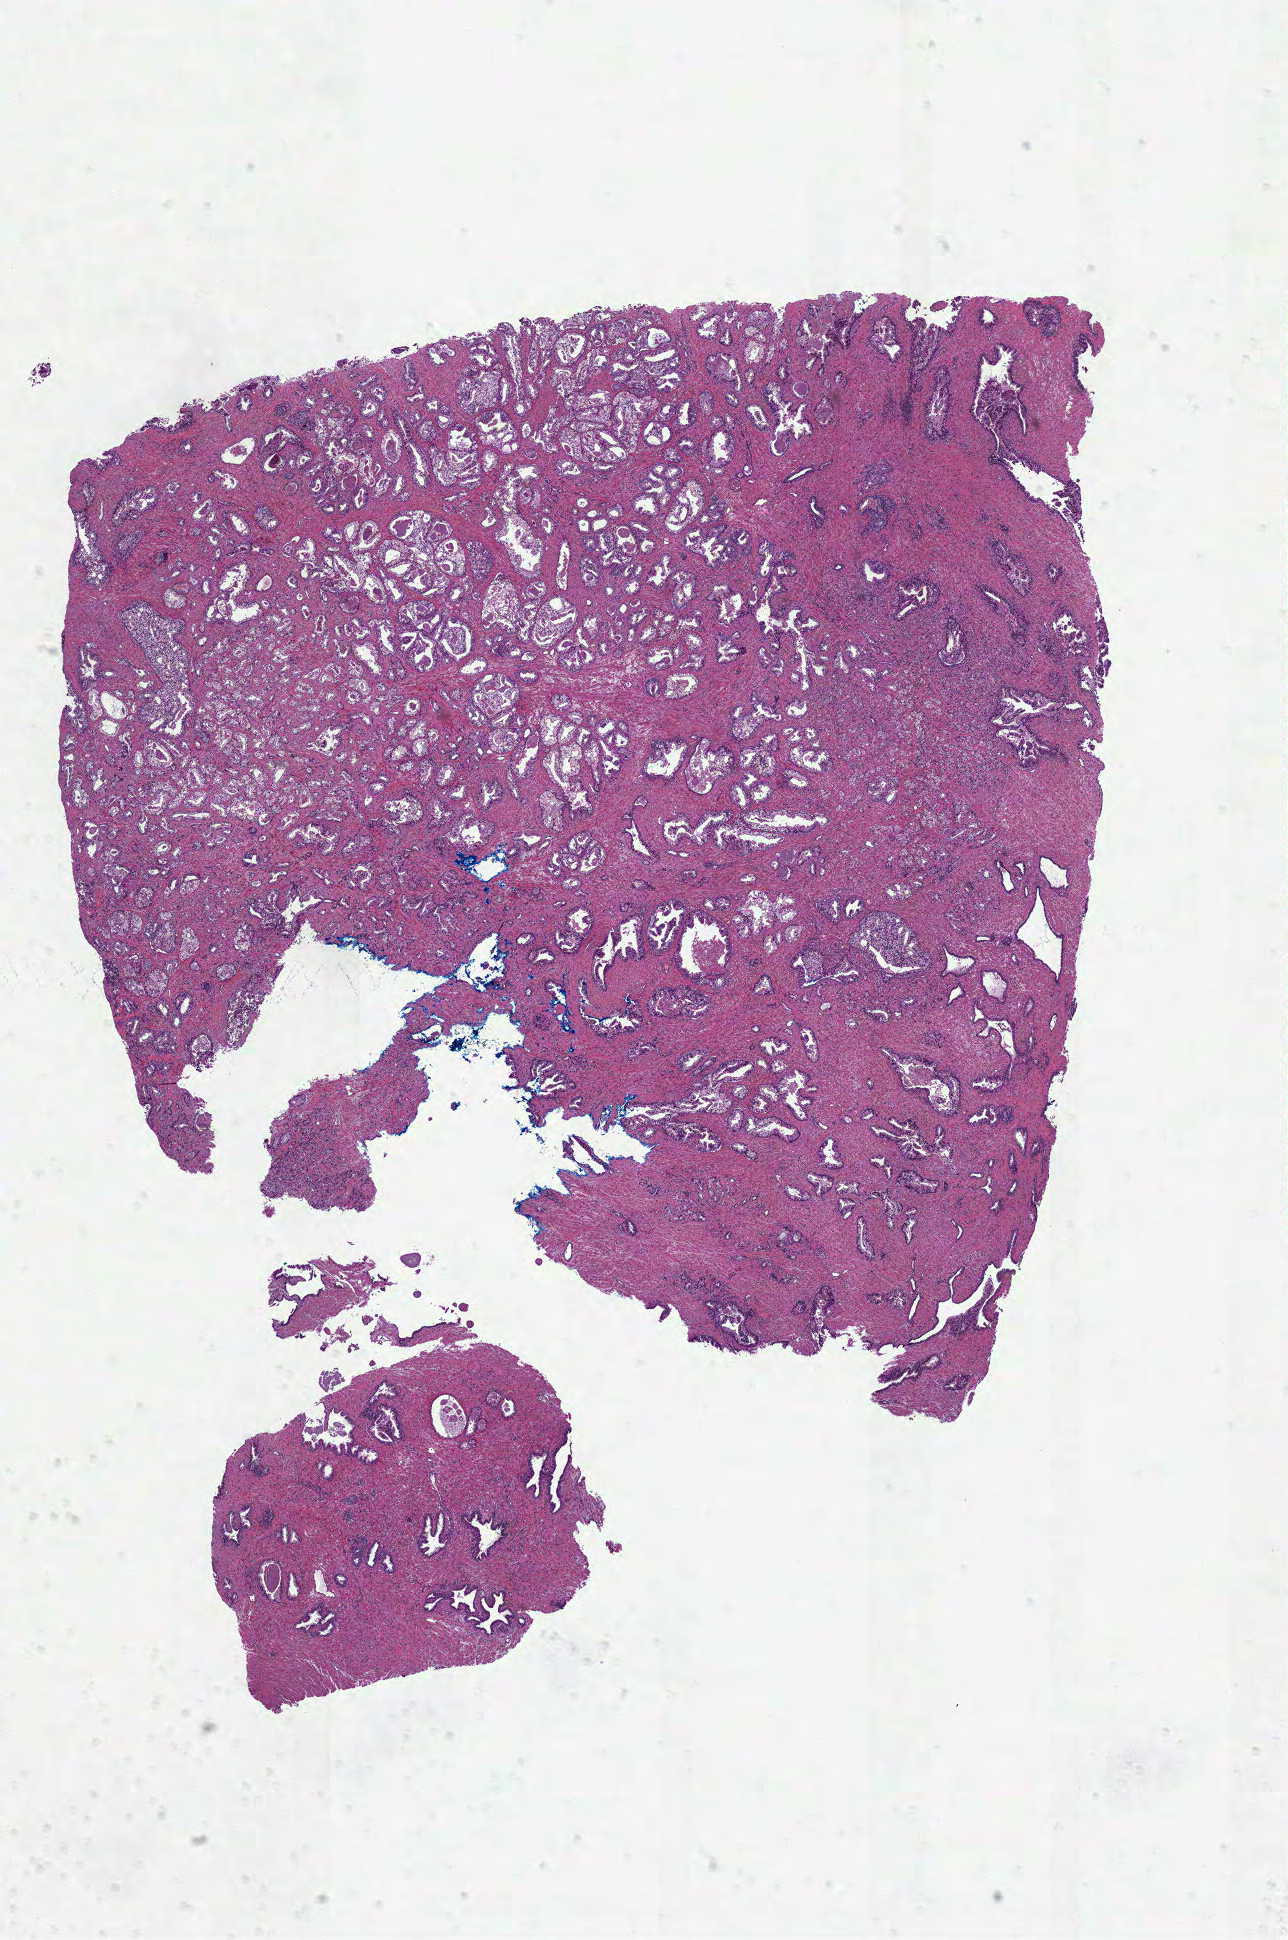
H&E-stained whole-slide image, shown as a low-resolution overview of the whole scanned area (about 10.4 x 15.7 mm, acquisition: 40x scan); formalin-fixed paraffin-embedded (FFPE) diagnostic section; primary tumour sample from the prostate. Patient: male, age at initial diagnosis 66 years. Gleason score: 9 (4+5).
* histologic diagnosis: Acinar cell carcinoma (prostate gland)